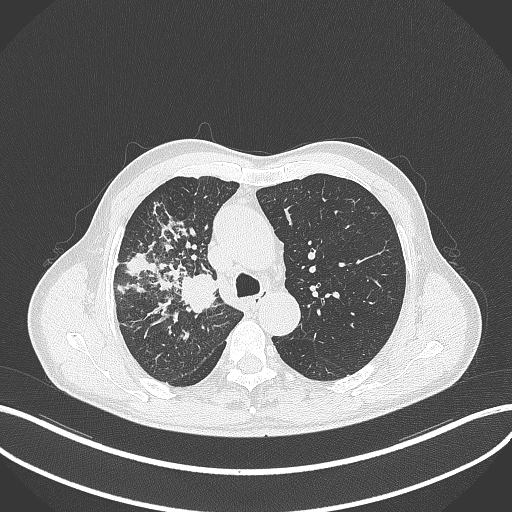
Chest CT, one axial slice; position 338 of 490 along the scan axis; lung window (W 1500 / L -600 HU); 512 × 512 image matrix. Male patient, age 69 years. Case-level facts recorded for this patient, not image findings: clinical TNM (as recorded): T2a N0 M0.
Outlined on this slice (rectangle marked by the reading radiologist):
- lung tumour (recorded histology: adenocarcinoma): box from (x=176, y=272) to (x=218, y=316) px